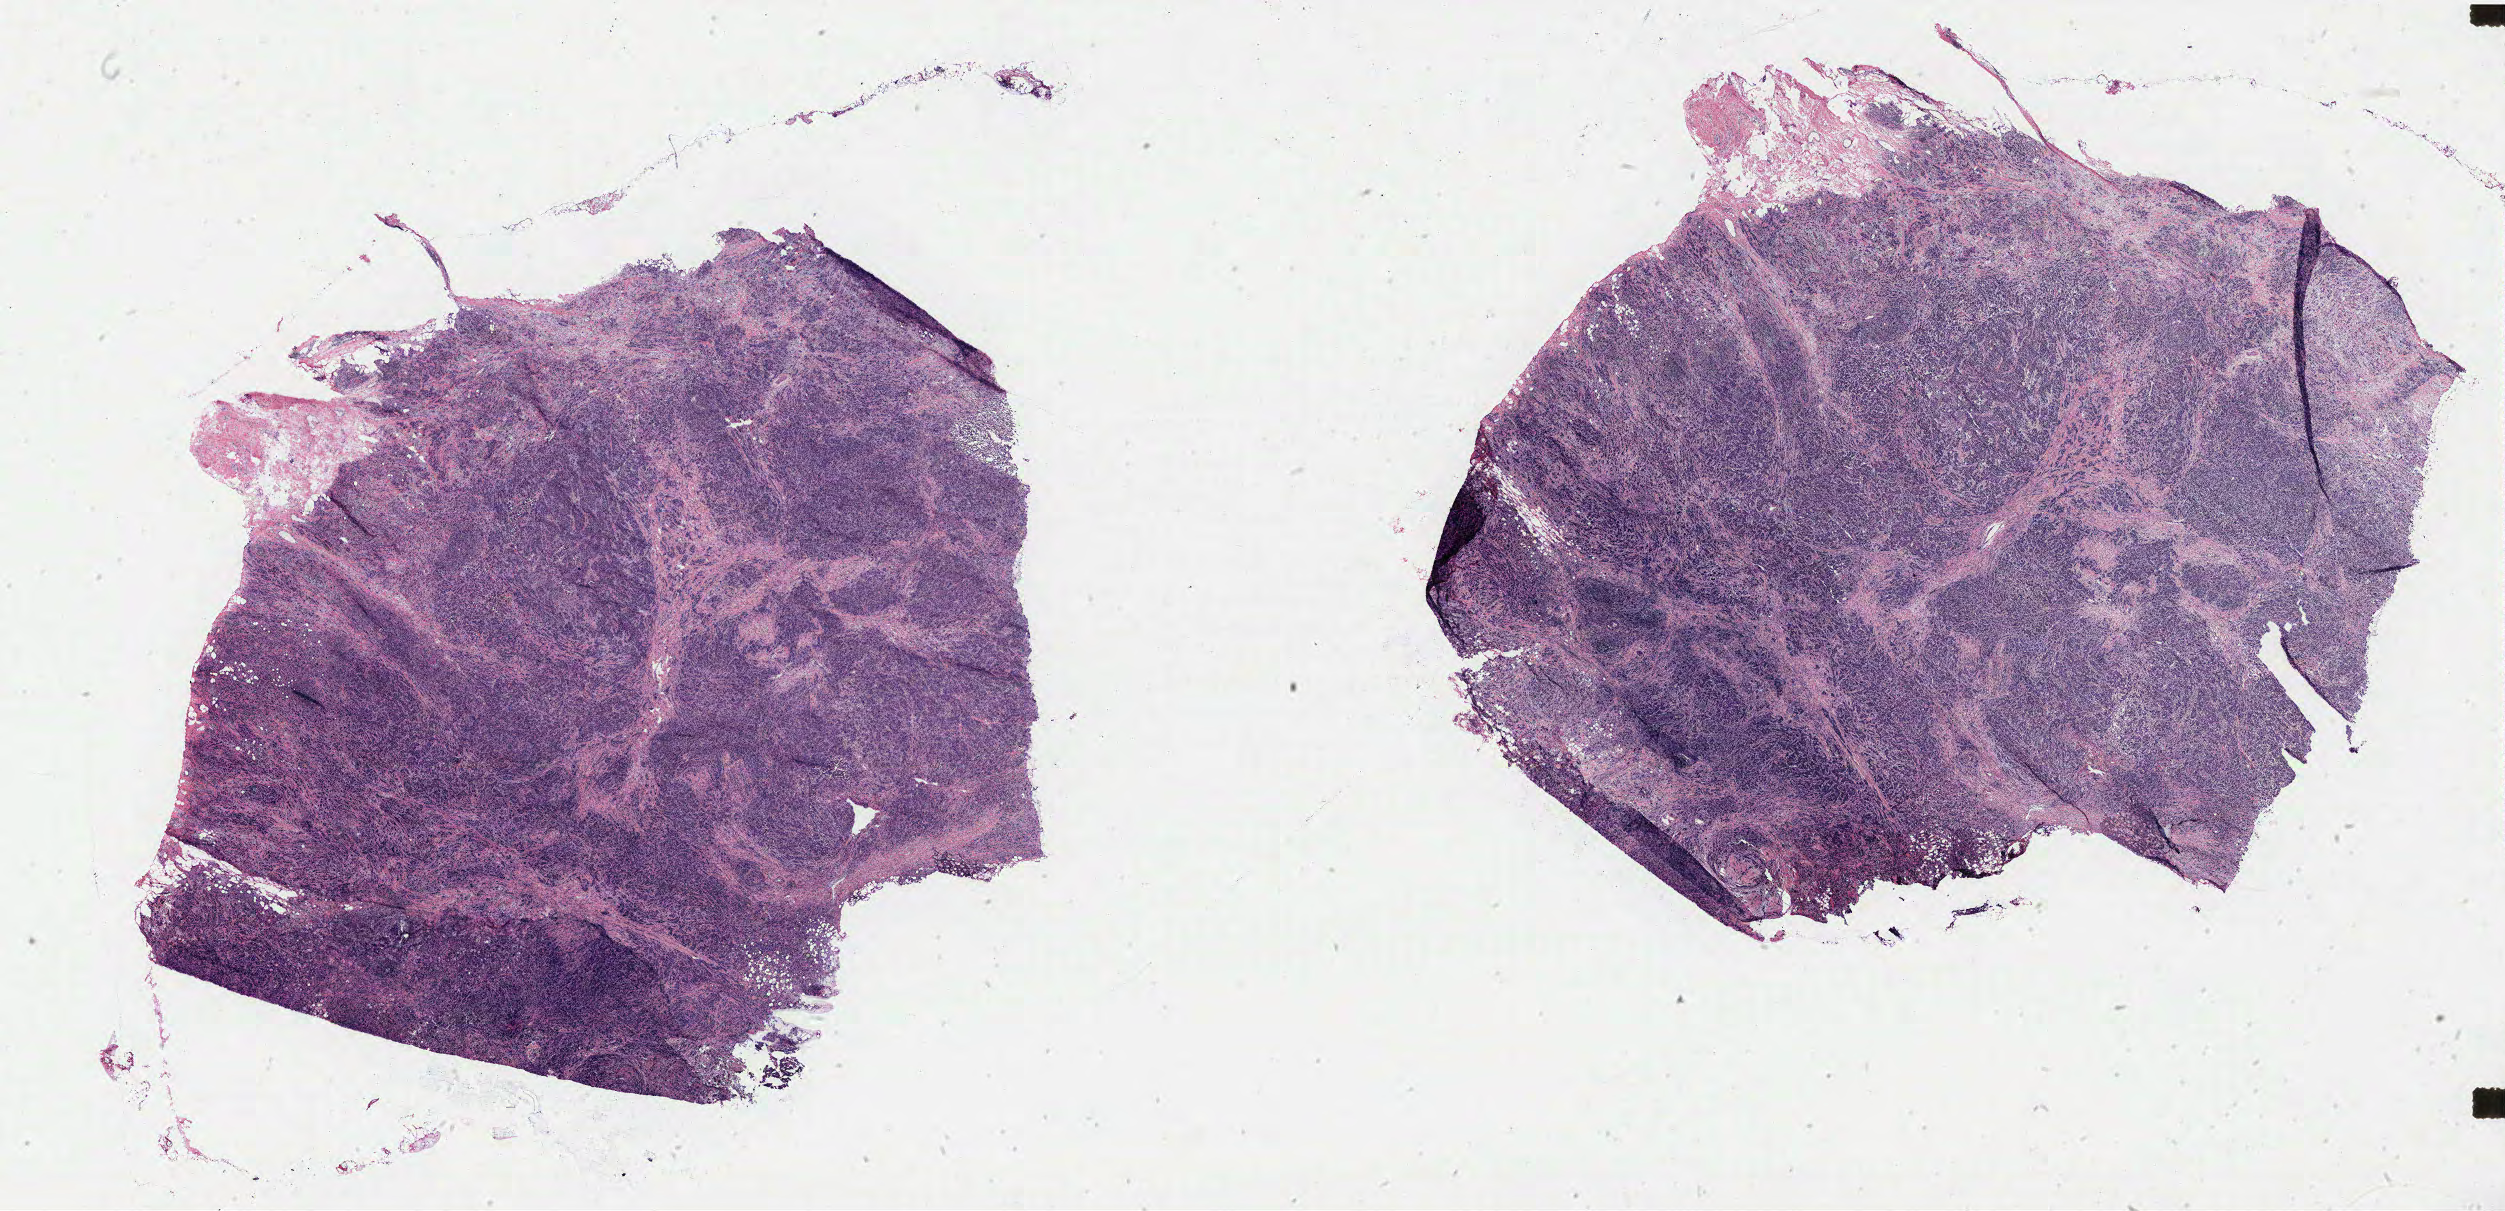
Whole-slide histology image, H&E — shown as a low-resolution overview of the whole scanned area (about 40.1 x 19.4 mm). Breast, tumour tissue. Patient: female, age 58 years.
Diagnosis: Infiltrating duct carcinoma, NOS. AJCC pathologic stage: IIA.